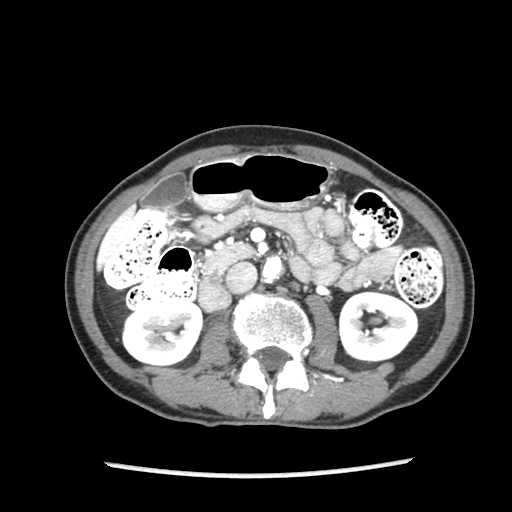
Contrast-enhanced abdominal CT (liver protocol), one axial slice; position 34 of 87 along the scan axis; soft-tissue window (W 400 / L 40 HU); 512 × 512 image matrix, field of view 300 × 300 mm. Case-level facts recorded for this patient, not image findings: diagnosis: hepatocellular carcinoma (patient treated with transarterial chemoembolisation; whether this scan precedes or follows treatment is not stated here); TNM stage (as recorded): Stage-IIIB; Child-Pugh class: A; tumour differentiation: well differentiated; tumour nodularity: uninodular.
Outlined on this slice (semi-automatically segmented with operator editing):
- liver parenchyma outside the tumour (the mass and vessels are separate outlines, so this box may not span the whole liver): bounding box <96,205,135,269> (left, top, right, bottom; pixels)